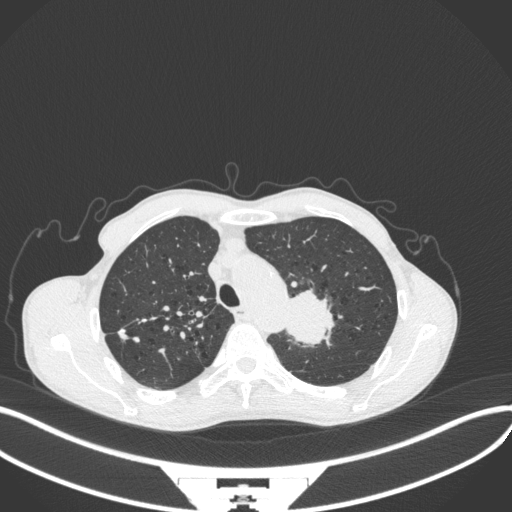
Chest CT, one axial slice. Position 323 of 394 along the scan axis. Reconstruction kernel B31f. Lung window (W 1500 / L -600 HU). 1 mm slice thickness. 512 × 512 image matrix, field of view 400 × 400 mm. Patient: male, 65 years. Case-level facts recorded for this patient, not image findings: clinical TNM (as recorded): T2b N0 M0; histopathological grade: G2.
Outlined on this slice (rectangle marked by the reading radiologist):
- lung tumour (recorded histology: adenocarcinoma): box from (x=278, y=283) to (x=341, y=350) px